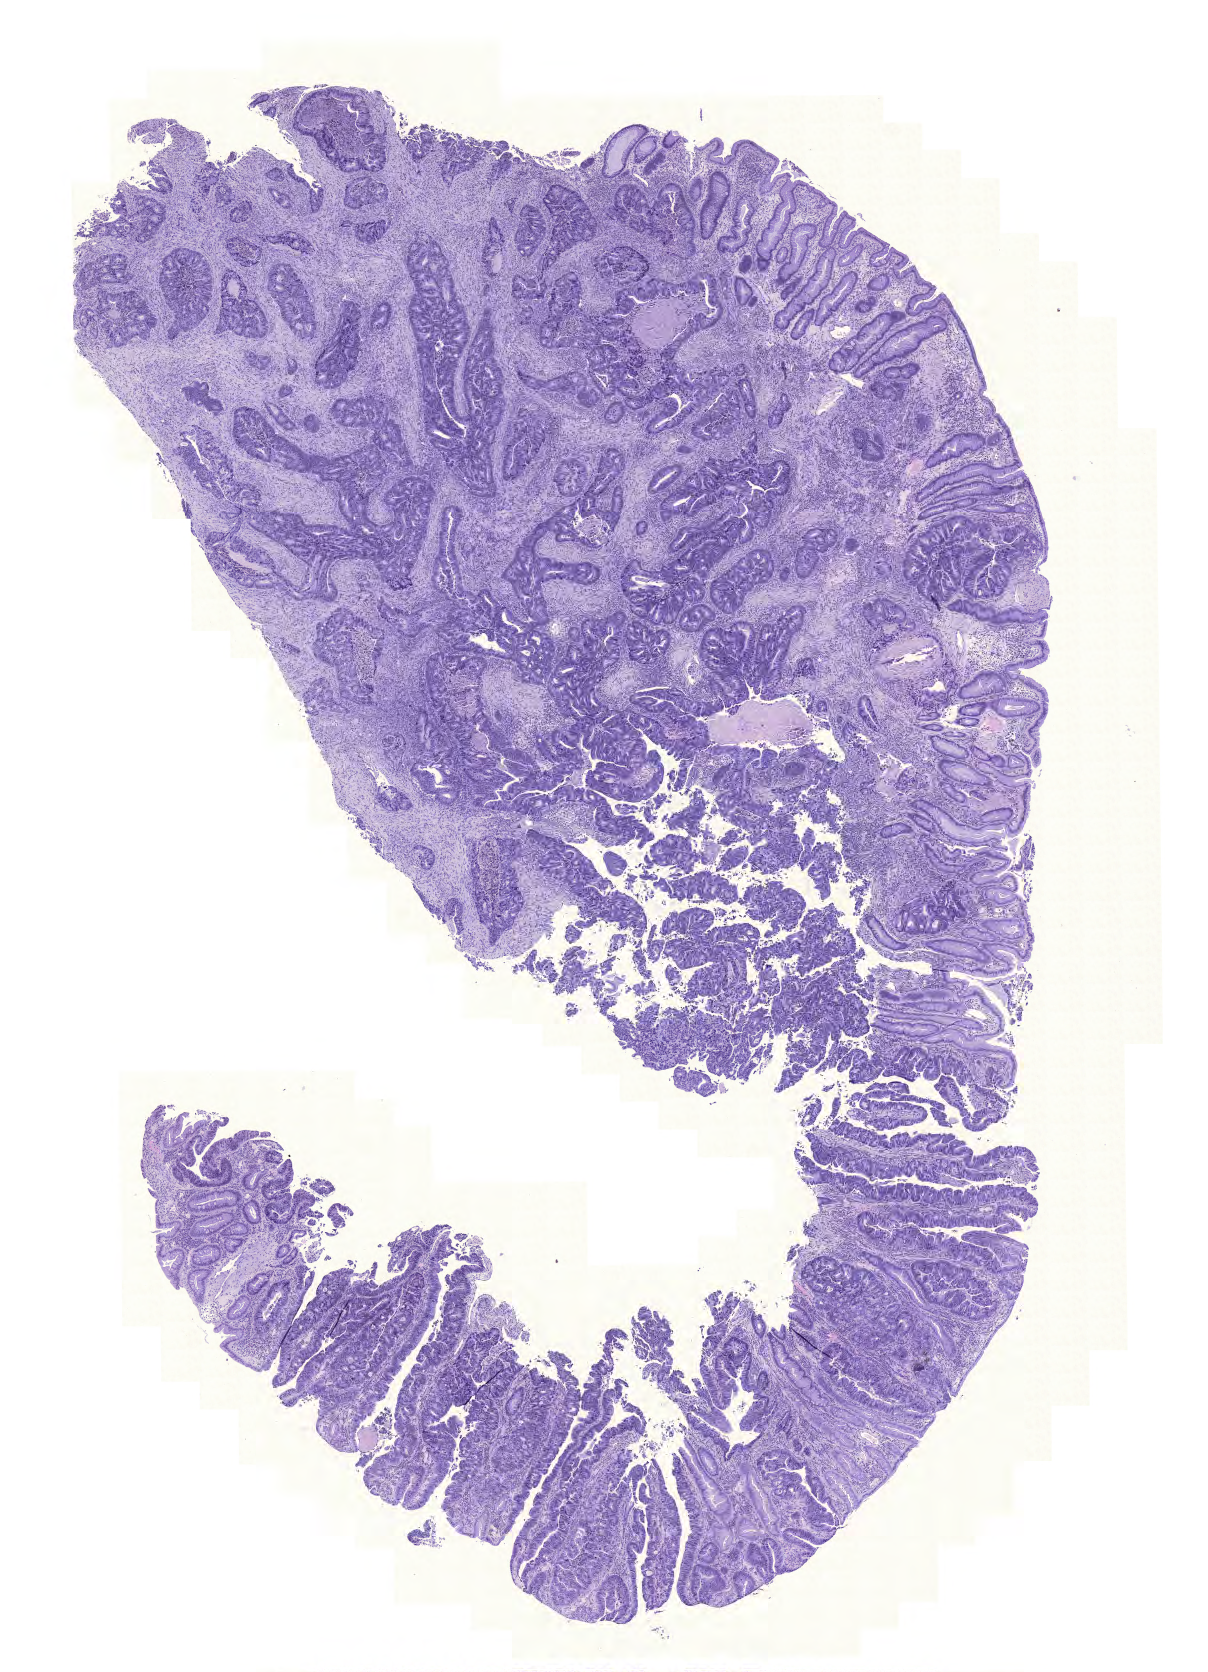
H&E whole-slide image — low-resolution overview of the scanned area, about 9.0 x 12.4 mm (acquisition: 20x scan), formalin-fixed paraffin-embedded (FFPE) diagnostic section, primary tumour sample from the colon. Male patient; age at initial diagnosis 75 years.
Pathologic diagnosis: Adenocarcinoma, NOS. AJCC pathologic stage: IIIB (6th edition). Lymph nodes positive (case pathology): 3 of 13 examined.